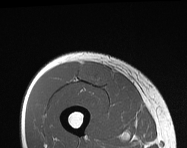
MRI of an extremity soft-tissue mass, one axial slice. Slice 48 of 114 in the series (ordered by position). MR volume resampled by the dataset authors to the PET/CT grid (not the native acquisition matrix). 3.27 mm slice thickness. 187 × 148 image matrix, field of view 183 × 145 mm. Male patient. From the clinical record (not read from this slice): histological type: pleiomorphic leiomyosarcoma; grade: intermediate; site of the primary tumour: right thigh.
Structures marked on this image (expert contour drawn on MRI and transferred to this co-registered scan by the dataset authors):
- gross tumour volume including surrounding oedema: bounding box <79,61,112,85> (left, top, right, bottom; pixels)